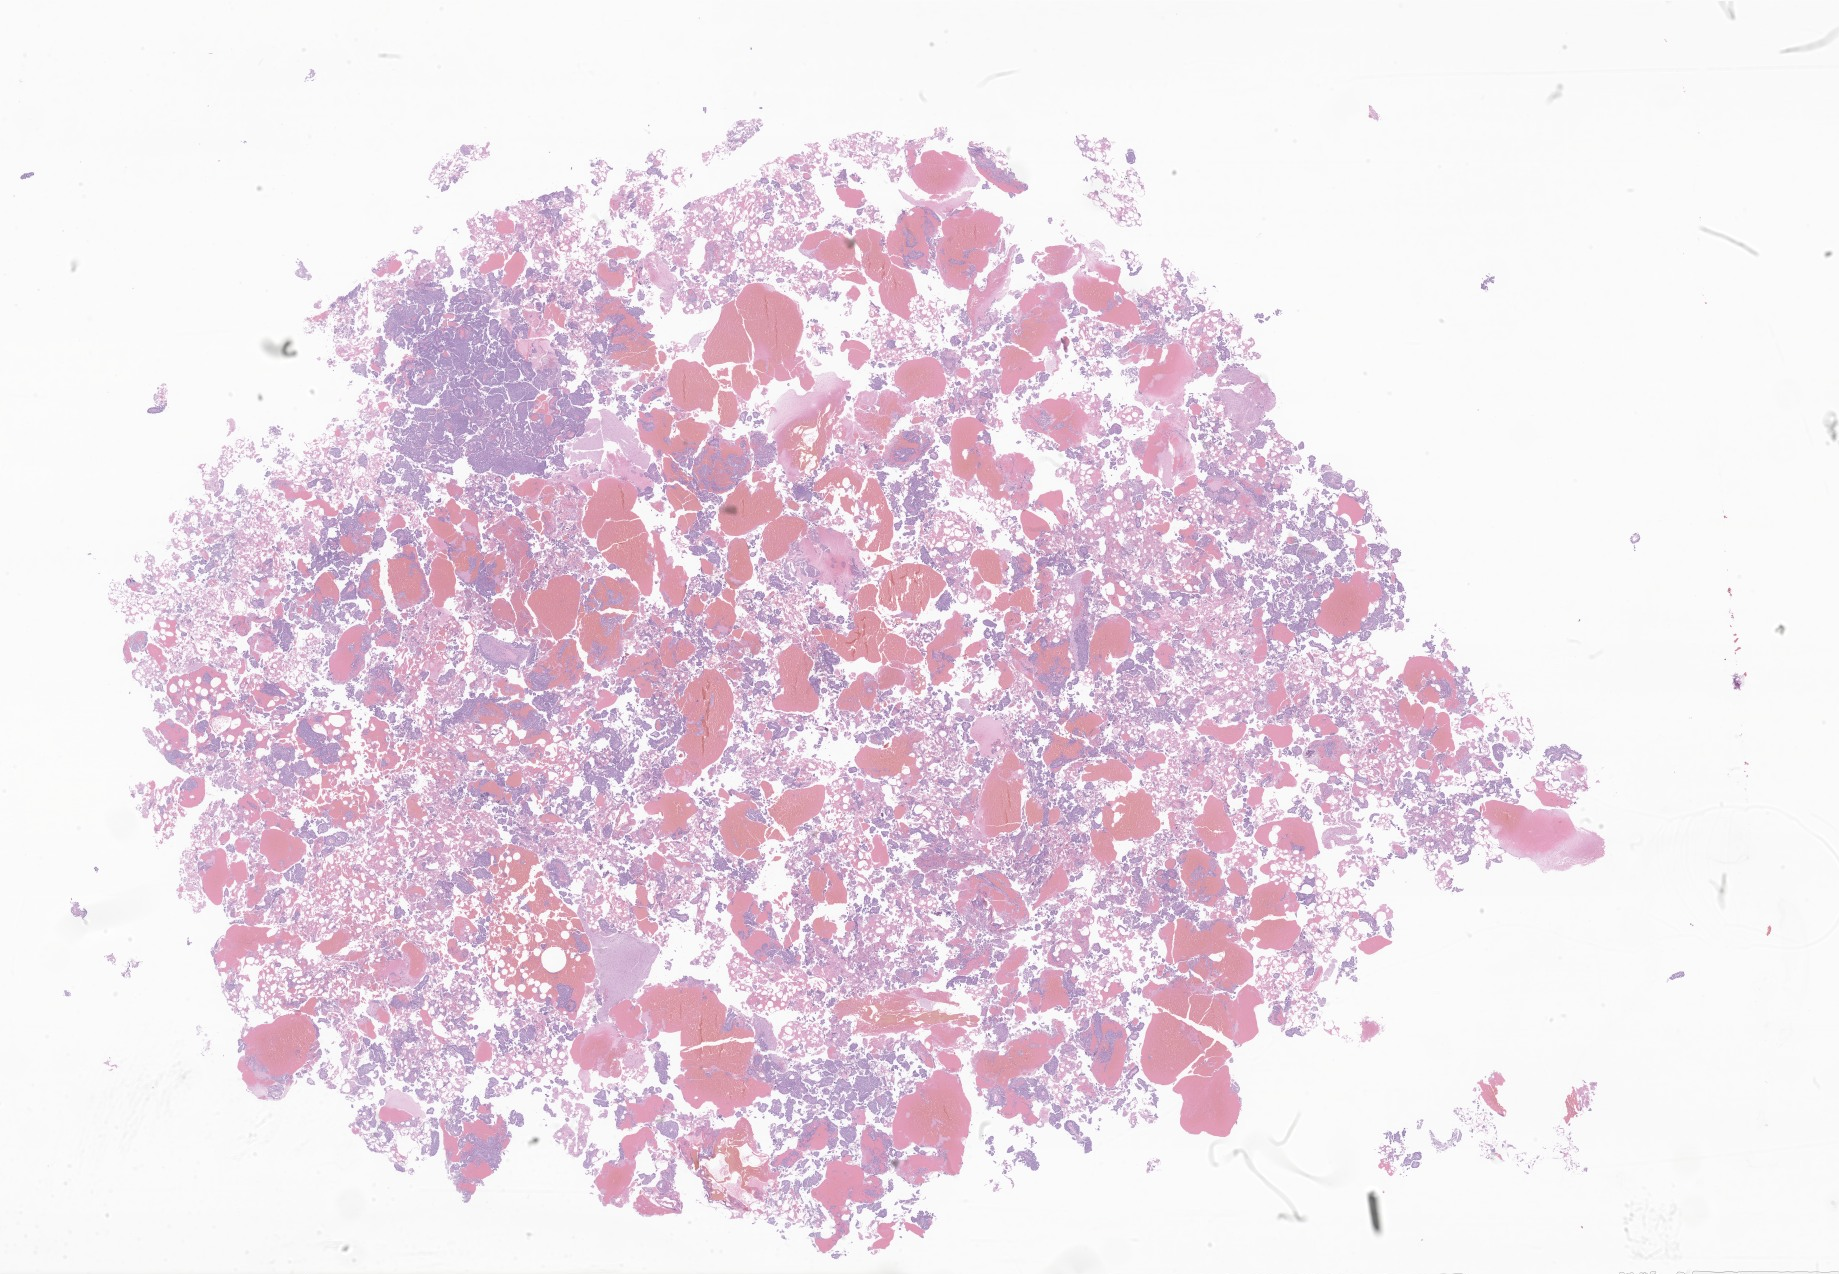
Haematoxylin and eosin whole-slide image of tumor tissue from the brain stem, whole scanned area (about 31.0 x 21.5 mm) shown as a low-resolution overview, FFPE section. Male patient, age 354 days.
- diagnosis: Choroid plexus carcinoma